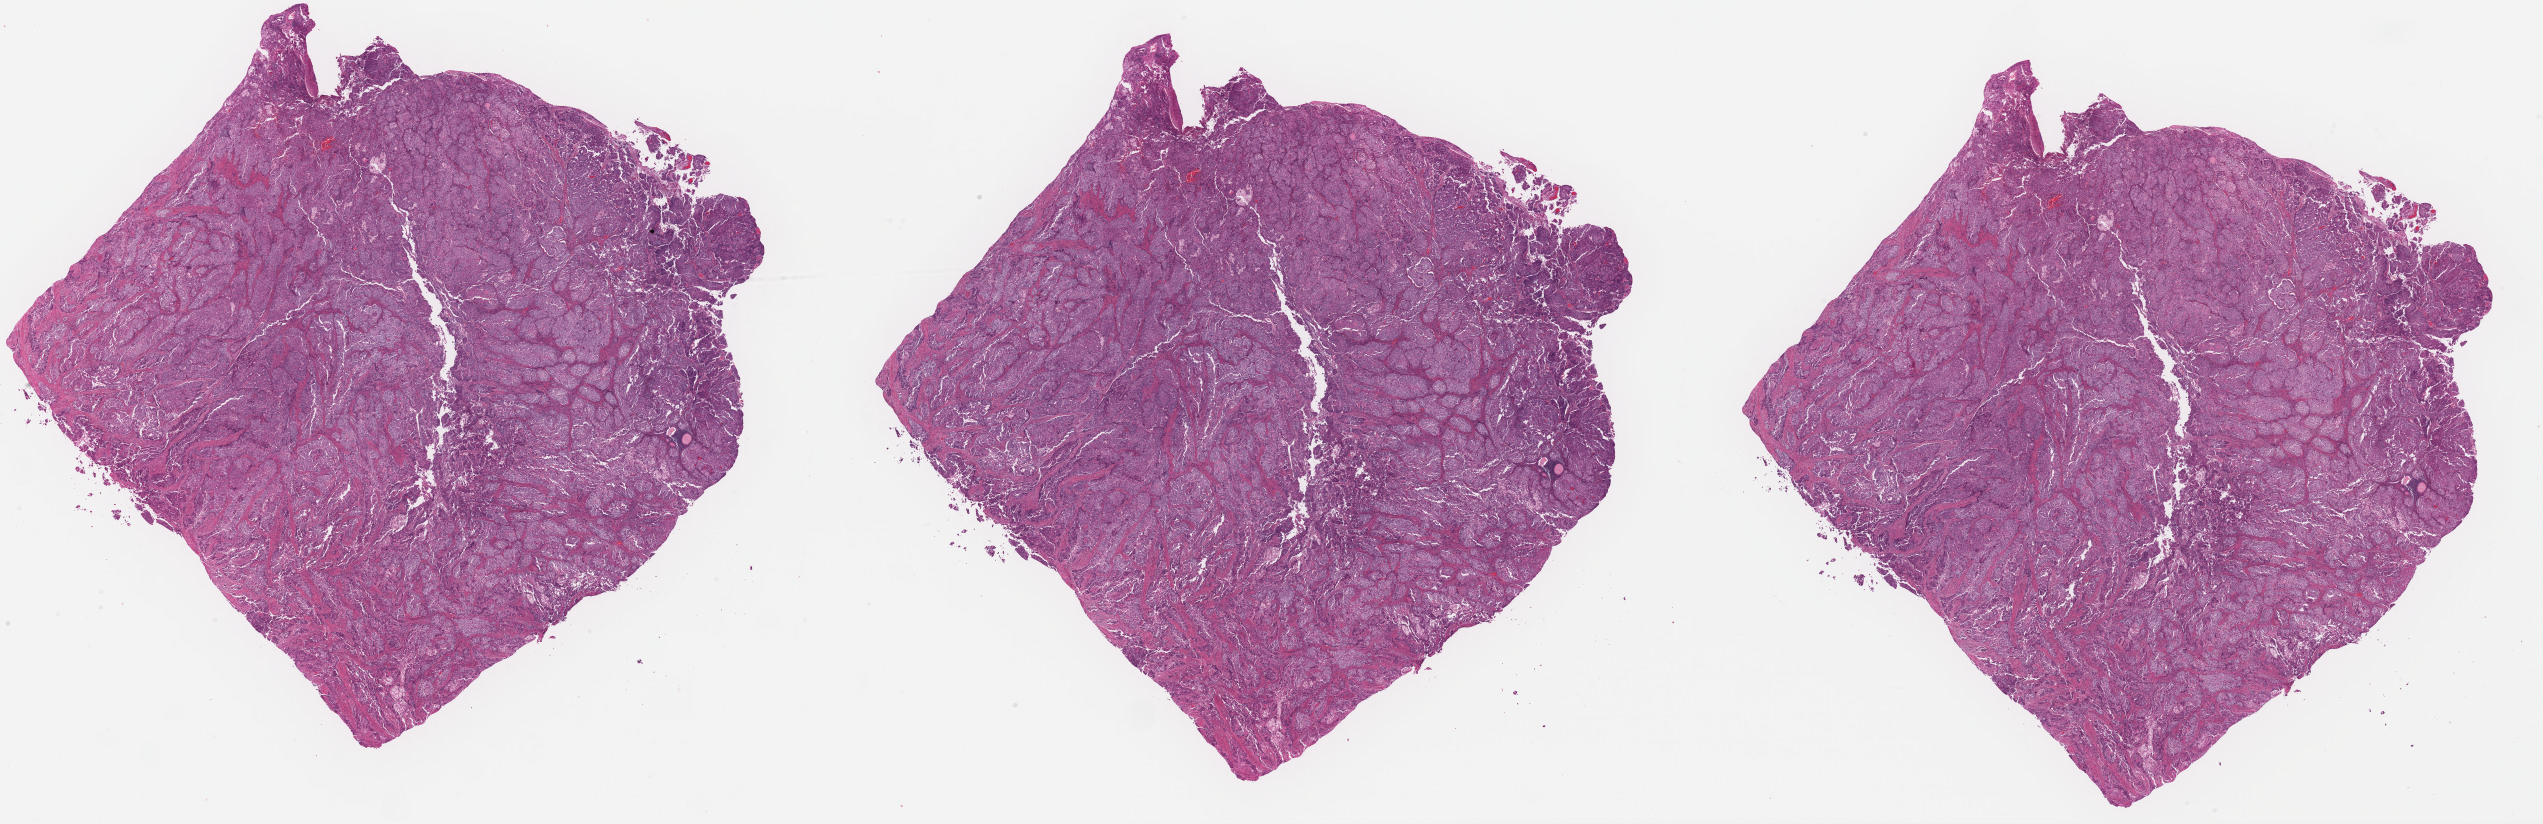
Digitized Hematoxylin and eosin (H&E) stained tissue section (whole slide) — a low-resolution overview of the entire scanned area, about 40.2 x 13.0 mm (slide scanned at 40x), FFPE section, sample: primary tumour, uterus. Female, age 76 years at initial diagnosis. Histologic grade: G3 (poorly differentiated).
Diagnosis: Endometrioid adenocarcinoma, NOS (endometrium). FIGO stage: IB.